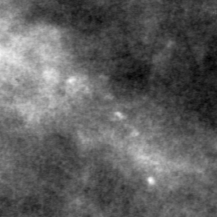
Crop from a digitized film mammogram around one marked abnormality, left breast, CC view.
- Finding: calcifications, morphology pleomorphic, distribution clustered; BI-RADS assessment category 4; subtlety rating 2 on a 1 (subtle) to 5 (obvious) scale; pathology (as recorded): benign.